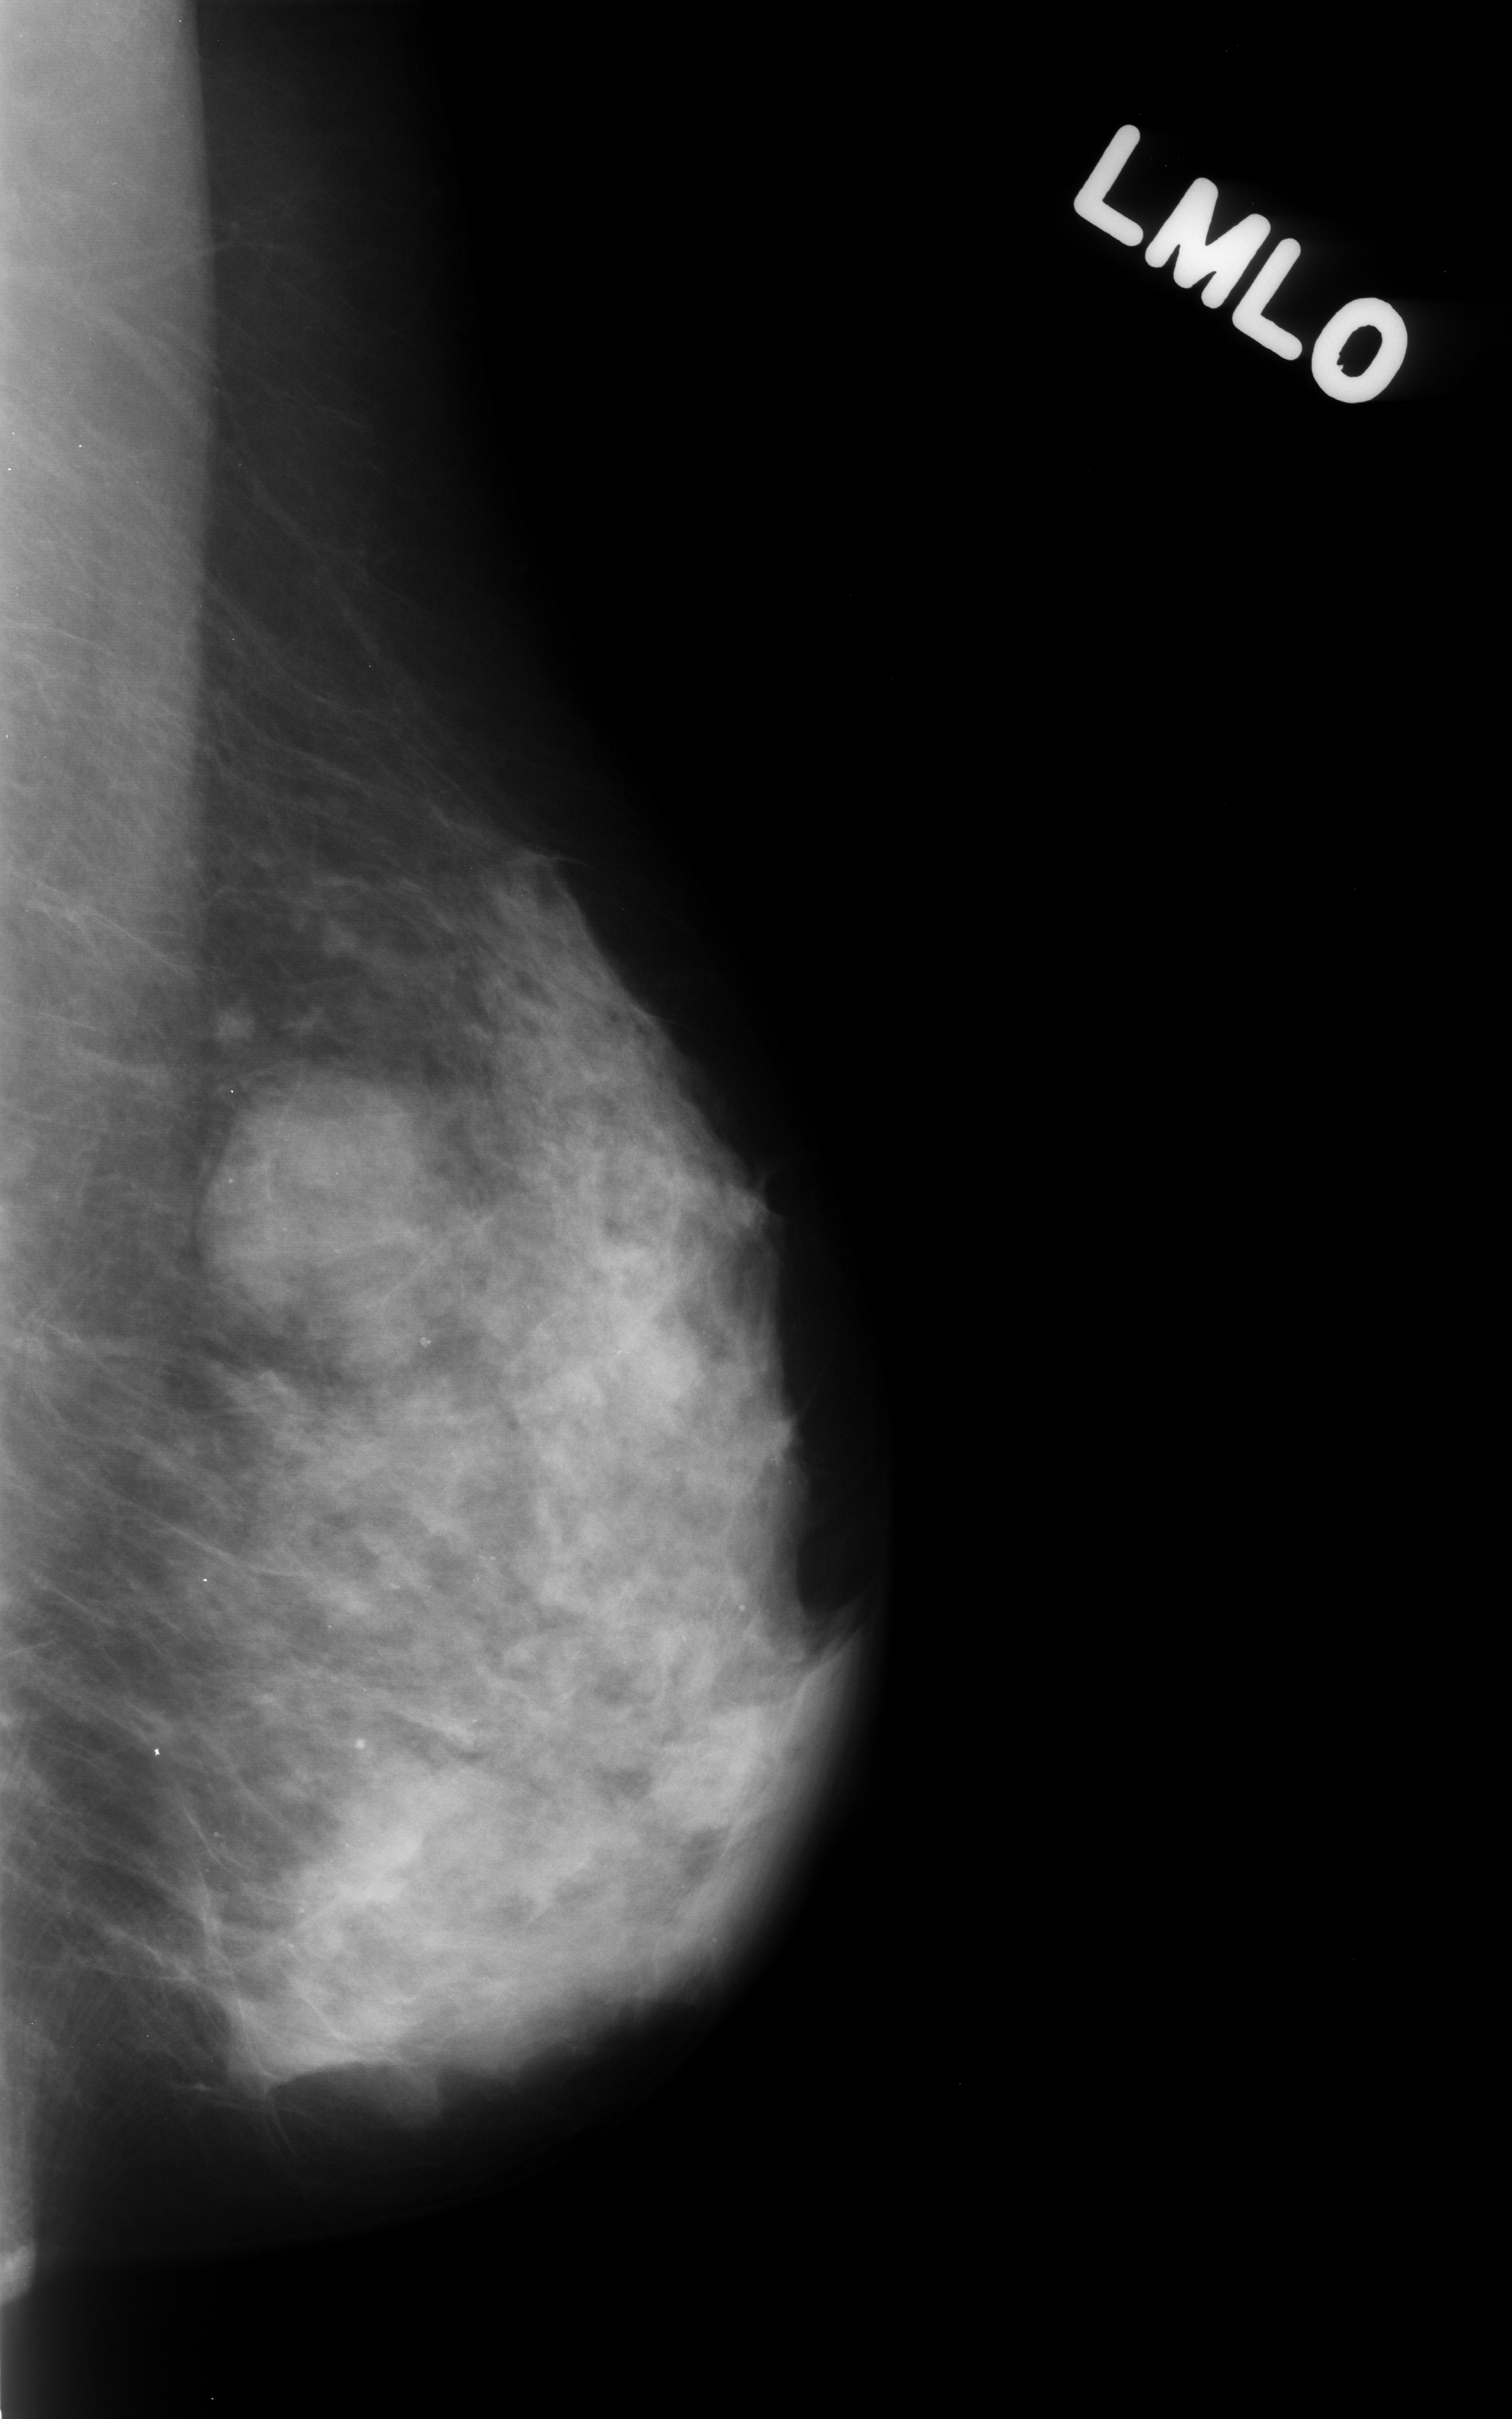
Mammogram (digitized film), left breast, MLO view.
Abnormality record for this image: mass, shape lobulated, margins obscured; BI-RADS assessment category 4; pathology (as recorded): benign.